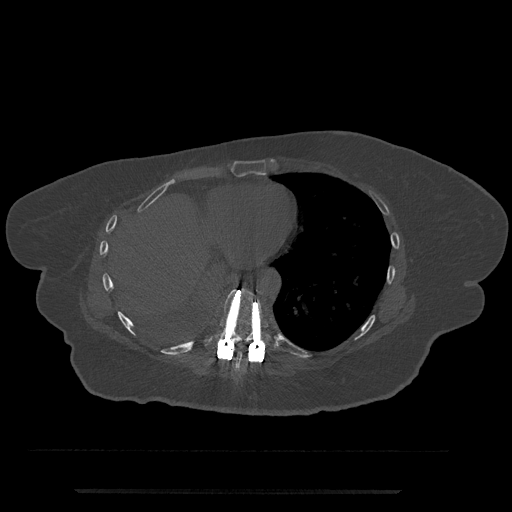
CT including the spine, one axial slice; position 351 of 797 along the scan axis; reconstruction kernel Br40s/3; 120 kVp; bone window (W 1800 / L 400 HU); 512 × 512 image matrix, field of view 440 × 440 mm. Female patient, age 51 years. From the clinical record (not read from this slice): primary cancer: neuro; vertebrae with lytic lesions (as recorded): T8.
Outlined on this slice (semi-automatically segmented with operator editing):
- T8 vertebra: bounding box [x1, y1, x2, y2] px = [231, 344, 250, 373]
- T9 vertebra: [204, 288, 277, 362]